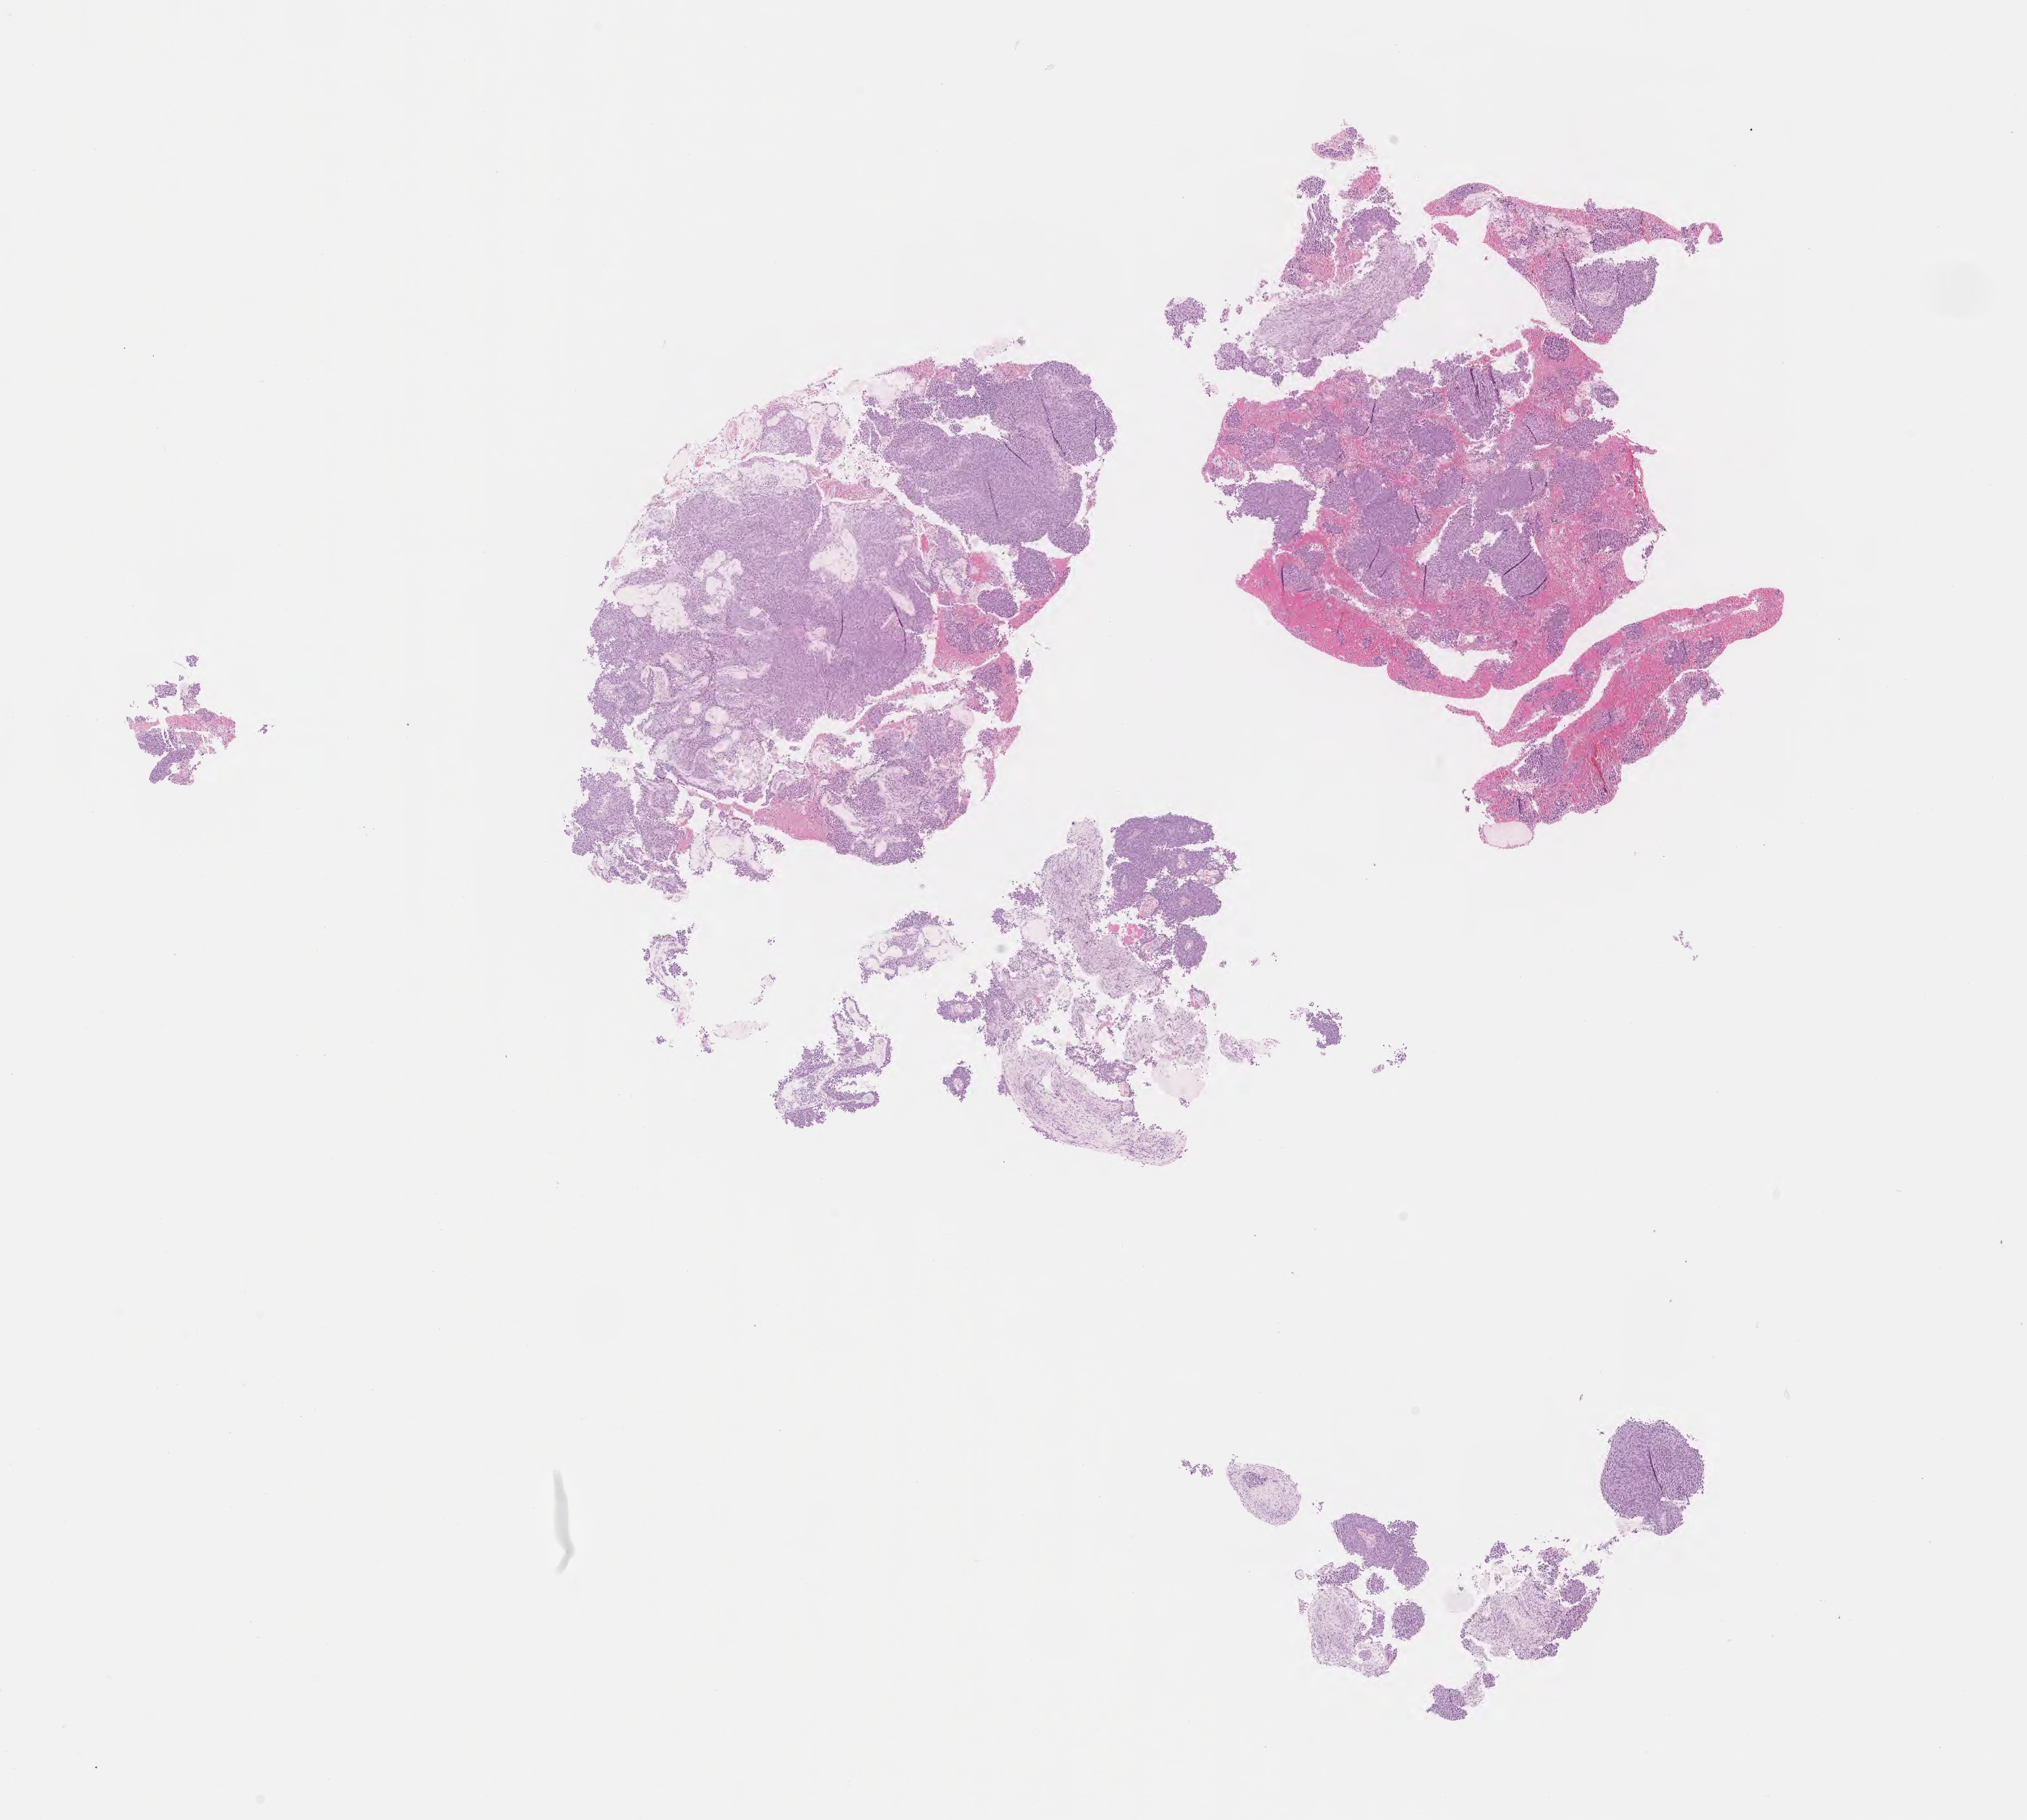
Digitized hematoxylin and eosin (H&E)-stained section, whole scanned area (about 12.6 x 11.3 mm) shown as a low-resolution overview, specimen: tumor tissue, anatomic site: cervix. Female patient, aged 44.
Histologic diagnosis: Squamous cell carcinoma, large cell, nonkeratinizing, NOS.